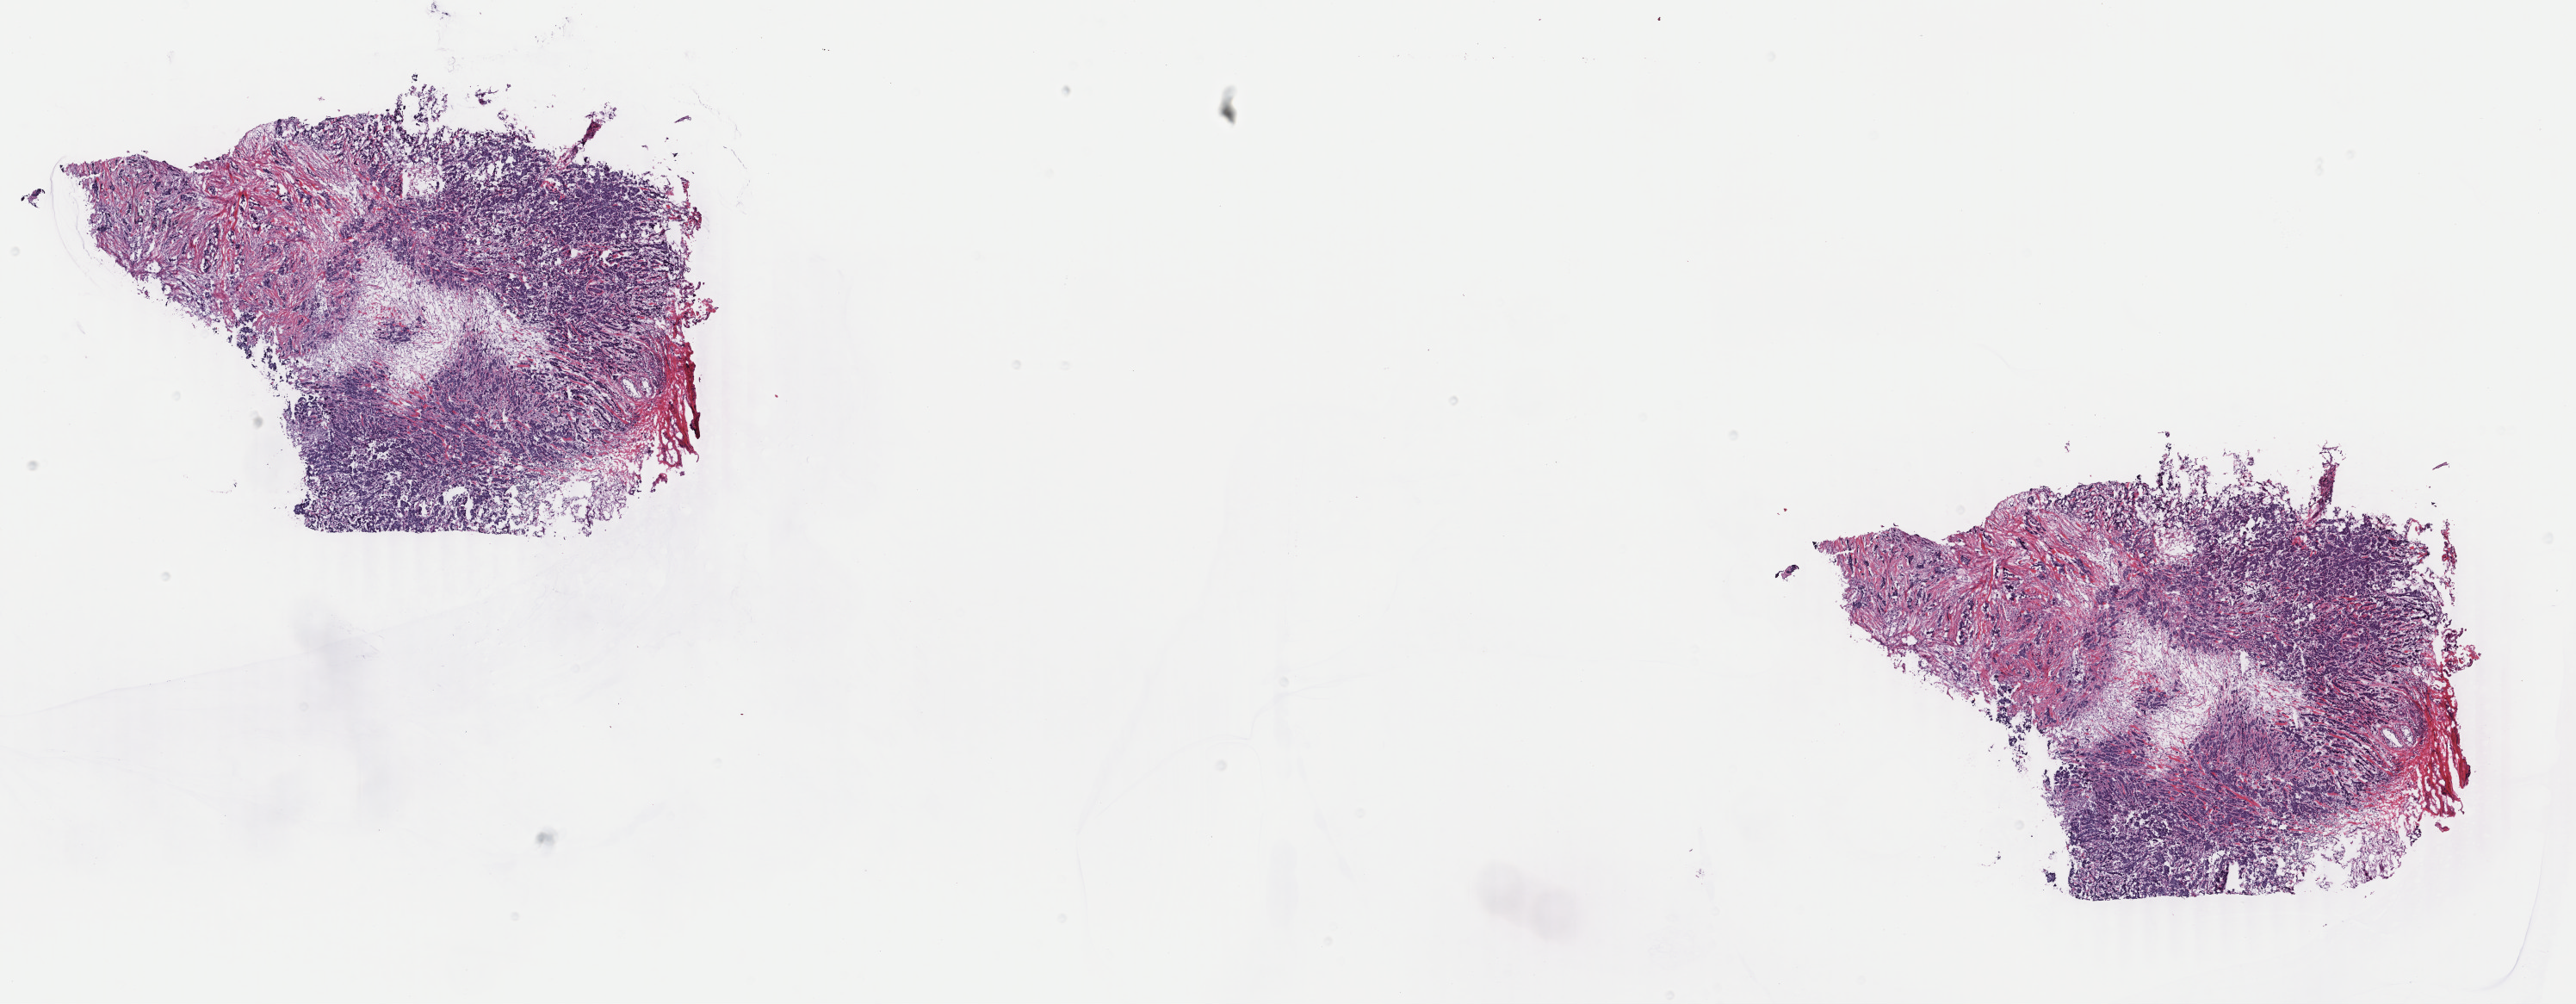
H&E whole-slide image, low-resolution overview of the scanned area, about 23.8 x 9.3 mm. Frozen section from the bottom of the tissue portion. Breast, primary tumour sample. Female, age 55 years at initial diagnosis. Composition of this section per pathologist review: tumour cells 90%, tumour nuclei 80%, normal cells 0%, stromal cells 10%, necrosis 0%. Inflammatory infiltration, as recorded: lymphocyte infiltration 0%, monocyte infiltration 0%, neutrophil infiltration 0%.
Pathologic diagnosis: Infiltrating duct carcinoma, NOS. Laterality: left. AJCC pathologic stage: IA. Lymph nodes positive (case pathology): 0 of 11 examined.